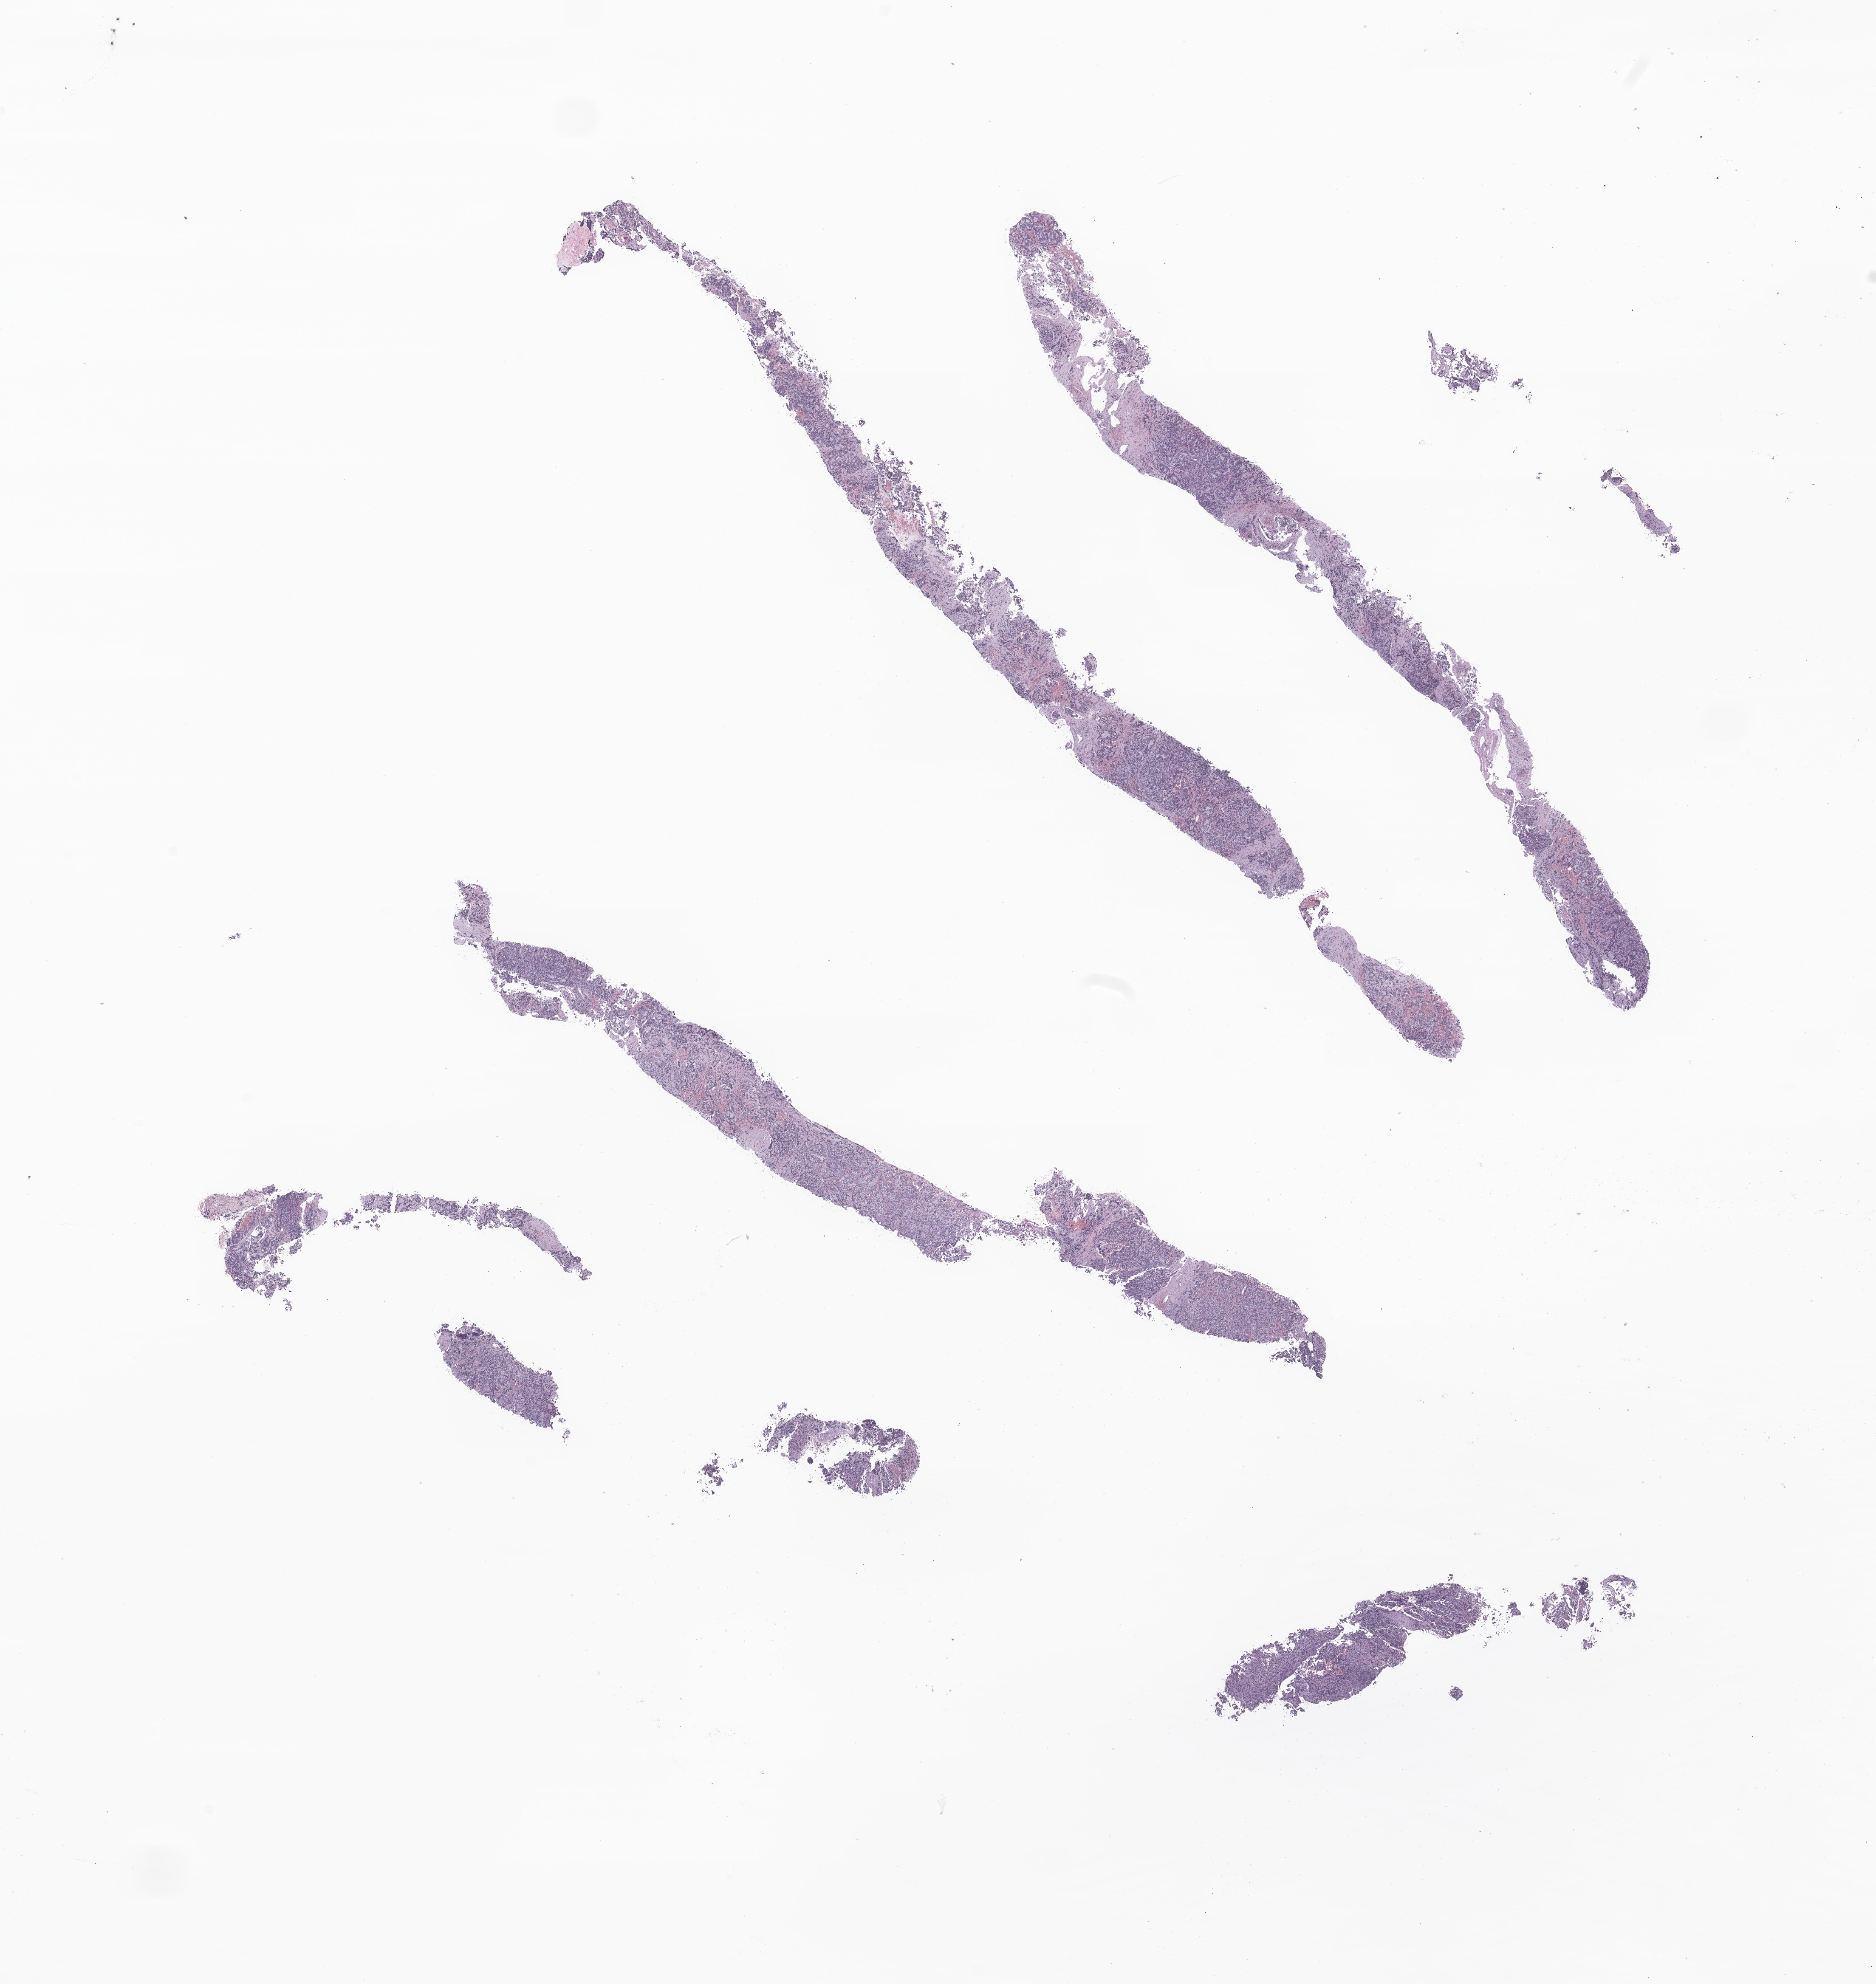
Whole-slide image, hematoxylin and eosin (H&E) stain of tumor tissue from the abdomen, a low-resolution overview of the entire scanned area, about 18.6 x 19.7 mm; formalin-fixed paraffin-embedded section. Patient: male, age 62 months.
* recorded diagnosis: Neuroblastoma, NOS